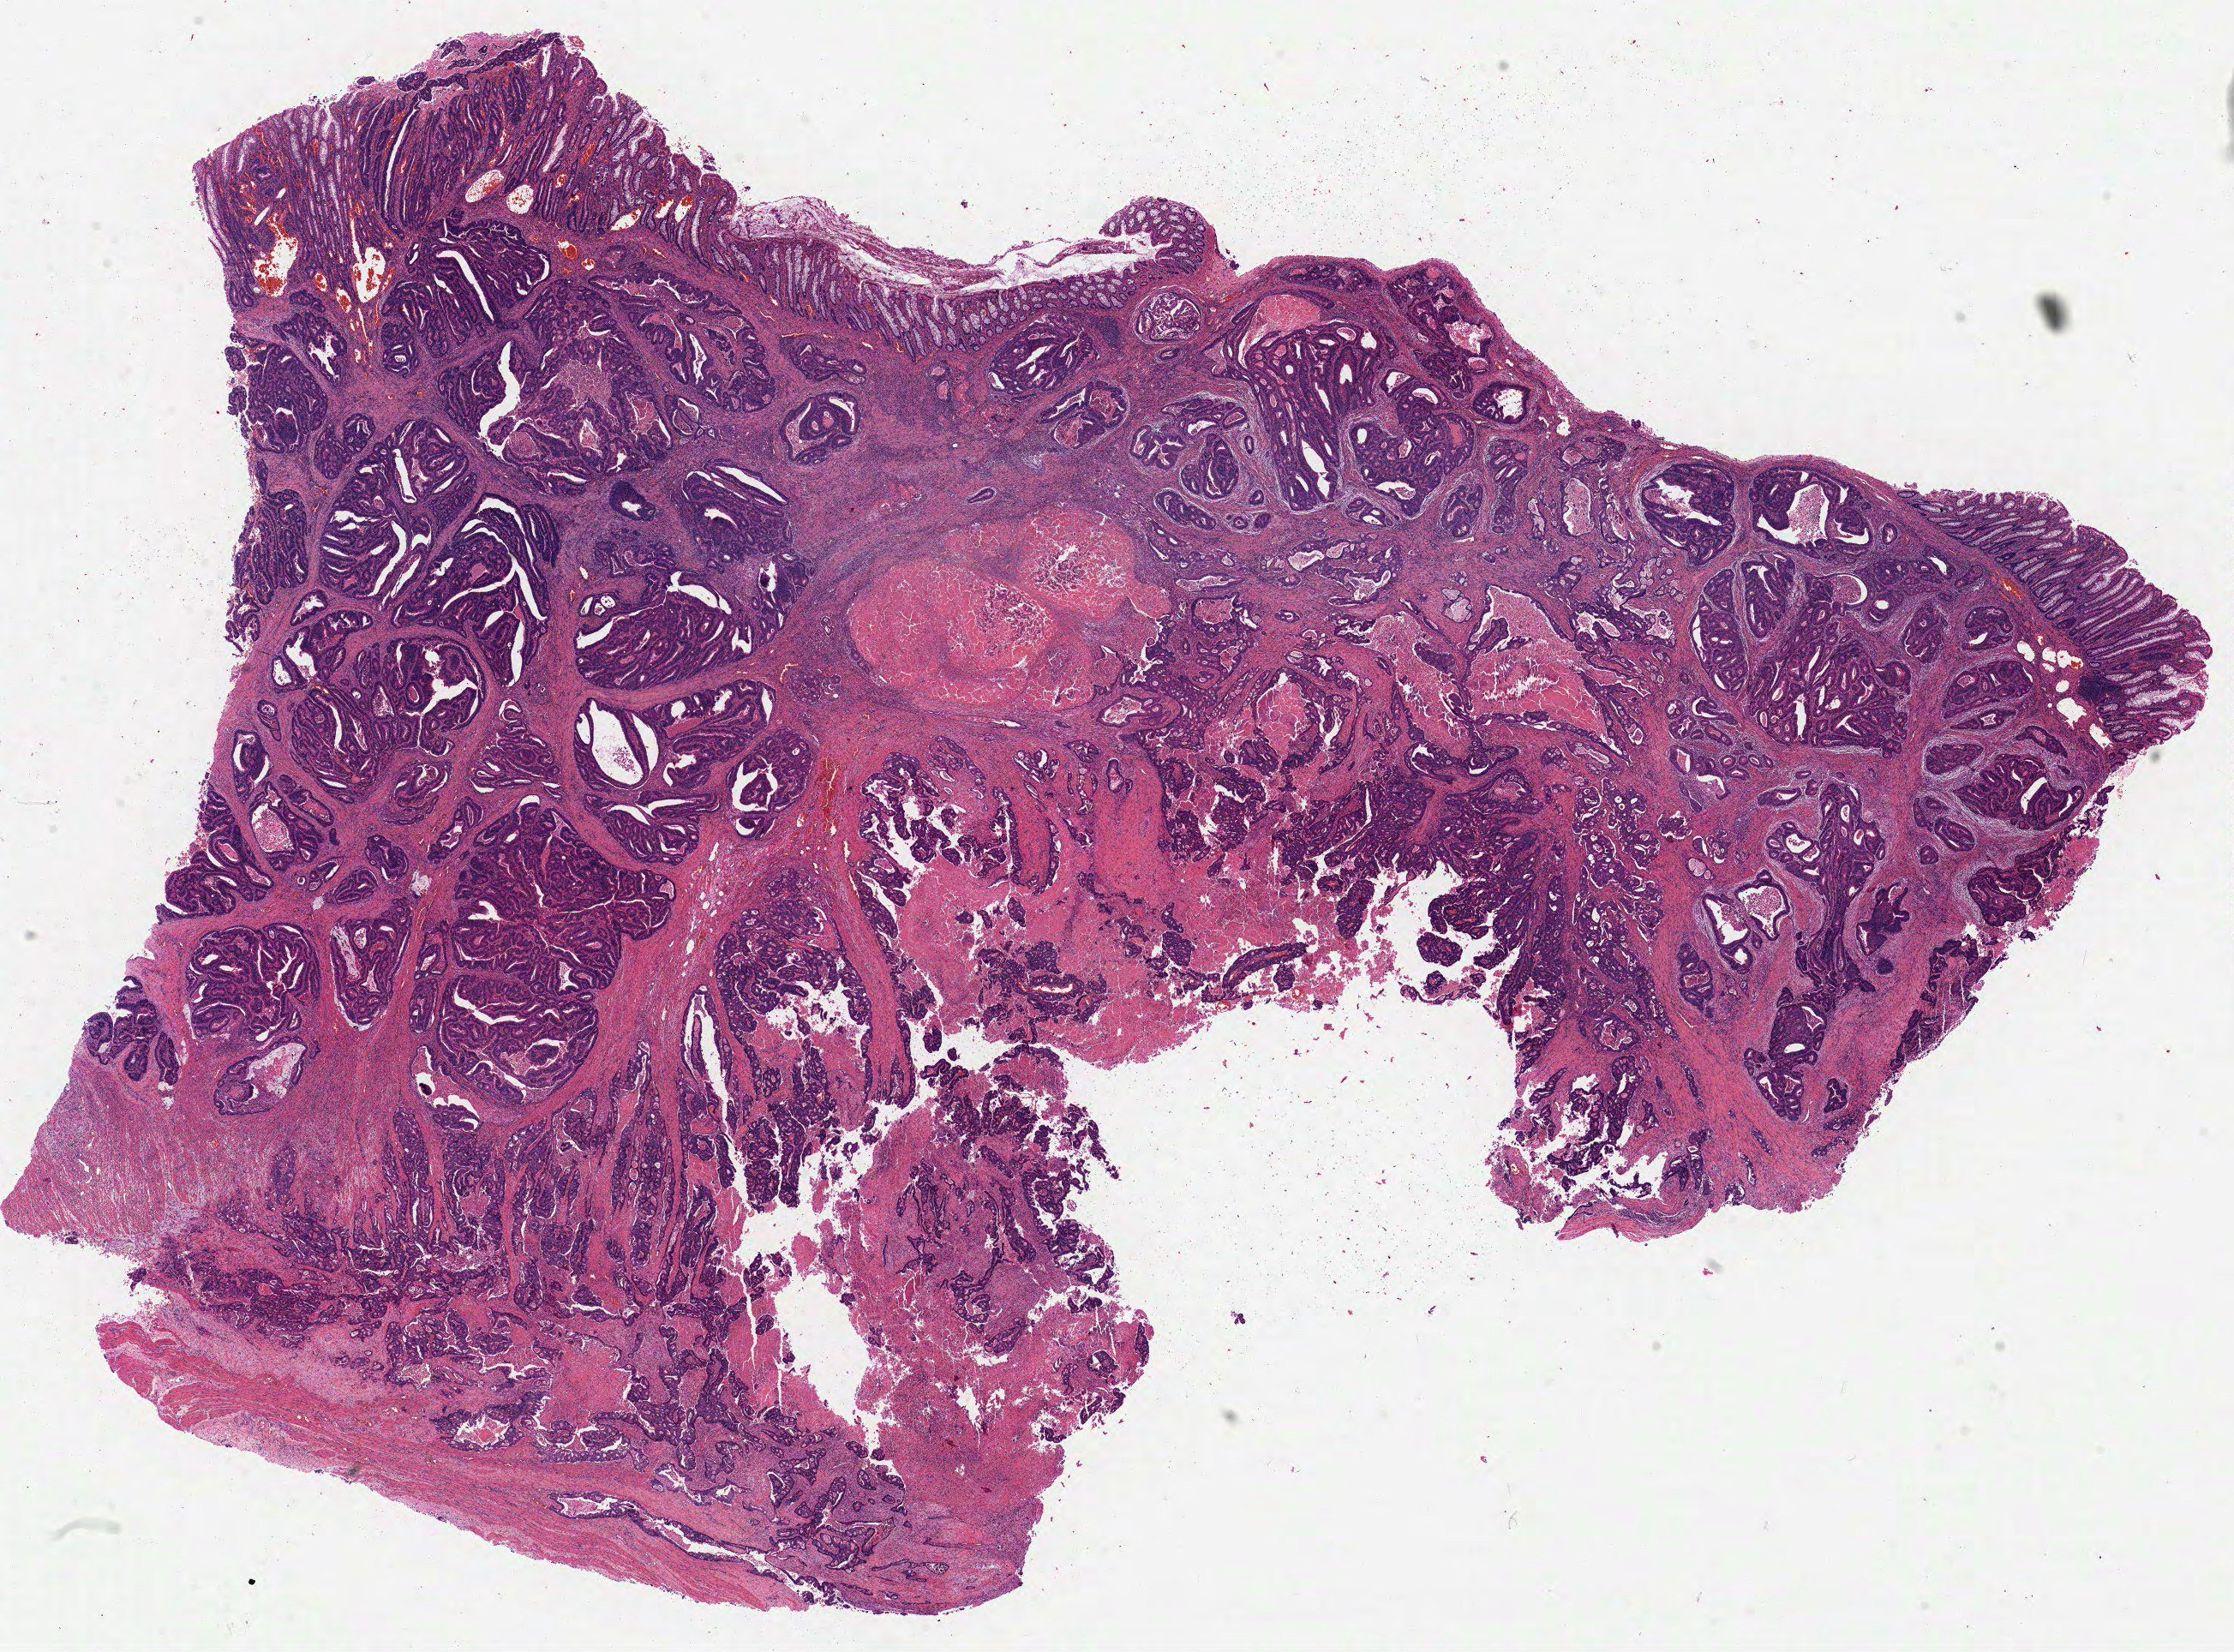
Whole-slide histology image, Hematoxylin and eosin (H&E) stained, a low-resolution overview of the entire scanned area, about 21.0 x 15.6 mm. Formalin-fixed paraffin-embedded (FFPE) diagnostic section. Sample: primary tumour, rectum. Male patient; age at initial diagnosis 54 years.
AJCC pathologic stage: IIB. Histologic diagnosis: Adenocarcinoma, NOS. TNM: T4a N0 M0.